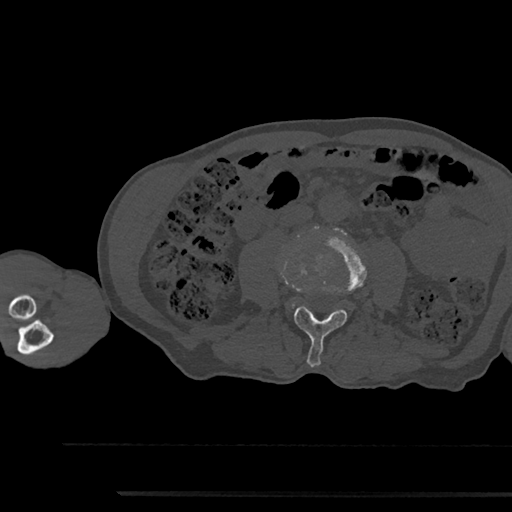
CT including the spine, one axial slice. Position 462 of 797 along the scan axis. Reconstruction kernel Br40s/3. 120 kVp. Bone window (W 1800 / L 400 HU). 512 × 512 image matrix, field of view 367 × 367 mm. Patient: male, 79 years. From the clinical record (not read from this slice): primary cancer: prostate.
Annotated regions visible in this slice (semi-automatically segmented with operator editing):
- L3 vertebra: bounding box <294,229,367,367> (left, top, right, bottom; pixels)